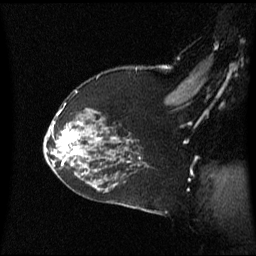
Breast MRI (dynamic contrast-enhanced), one sagittal slice. Slice 45 of 60 in the series (ordered by position). Dynamic contrast-enhanced series, image 2 of 3 at this slice position (ordered by acquisition). 1.5 T. TE 4.2 ms, TR 8.4 ms. 2 mm slice thickness. 256 × 256 image matrix. Patient: female, 59 years. Case-level facts recorded for this patient, not image findings: setting: breast cancer imaged before/during neoadjuvant chemotherapy; receptor status: HR-positive, HER2-negative.
Annotated regions visible in this slice (semi-automatic segmentation, software-assisted and operator-edited):
- analysis volume of interest (the breast-tissue region the enhancement analysis was run in; not a lesion): bounding box <46,122,89,163> (left, top, right, bottom; pixels)
- tumour enhancement mask (voxels above the 70 % enhancement threshold inside the analysis volume of interest): <63,130,79,155>